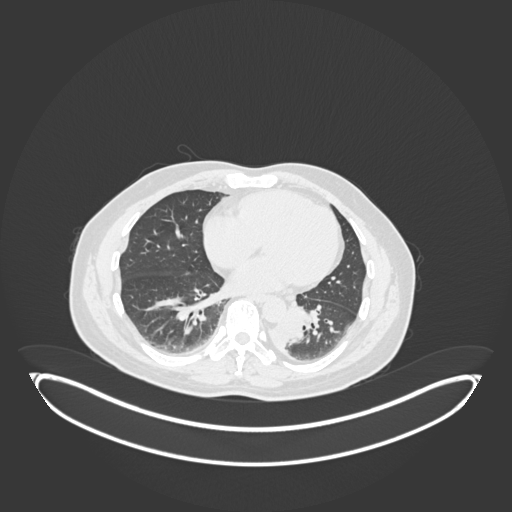
Chest CT, one axial slice; reconstruction kernel B30f; lung window (W 1500 / L -600 HU); 1 mm slice thickness; 512 × 512 image matrix, field of view 500 × 500 mm. Patient: male, 54 years. From the clinical record (not read from this slice): clinical TNM (as recorded): T3 N0 M0.
Outlined on this slice (bounding box drawn by a radiologist):
- lung tumour (recorded histology: squamous cell carcinoma): bounding box [x1, y1, x2, y2] px = [270, 311, 308, 349]